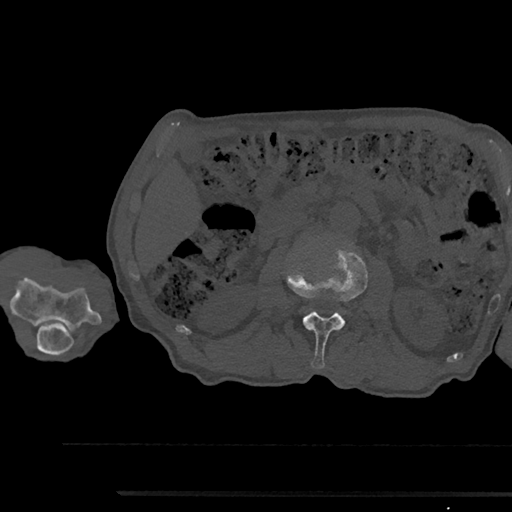
CT including the spine, one axial slice; slice 548 of 797 in the series (ordered by position); reconstruction kernel Br40s/3; 120 kVp; bone window (W 1800 / L 400 HU); 0.5 mm slice thickness; 512 × 512 image matrix. Patient: male, 79 years. Case-level facts recorded for this patient, not image findings: primary cancer: prostate.
Annotated regions visible in this slice (semi-automatic segmentation, software-assisted and operator-edited):
- L2 vertebra: bounding box [x1, y1, x2, y2] px = [287, 246, 367, 369]